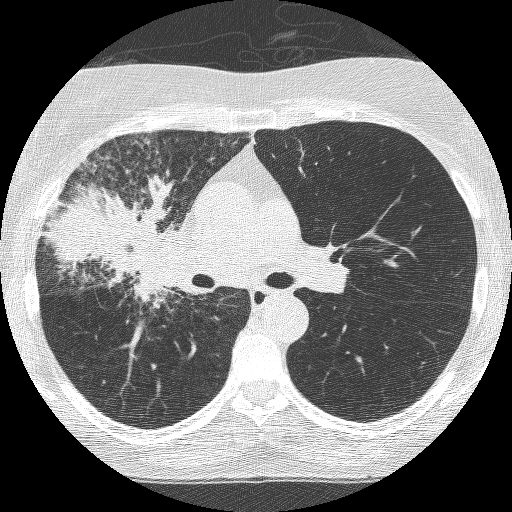
Axial slice from a low-dose chest CT screening exam; third screening round (two years after baseline); lung window (W 1500 / L -600 HU); 120 kVp; slice 157 of 253 in the series. Female, age 64 years at enrolment. Former smoker at enrolment.
Expert-annotated lung lesion, bounding box <75,196,203,325> (left, top, right, bottom; pixels). Reader record for this screening exam (exam-level; its link to the box is not recorded): non-calcified nodule or mass ≥4 mm, right upper lobe, 49 × 43 mm, spiculated (stellate) margins, soft tissue attenuation, pre-existing on the prior screen: yes; interval growth: yes. Official screen result: positive, other.